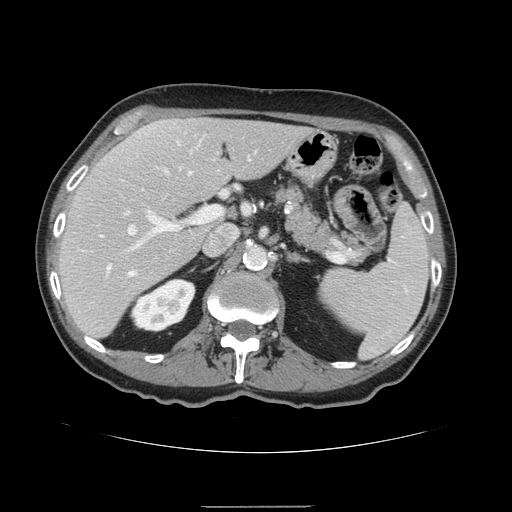
Contrast-enhanced abdominal CT, one axial slice. Slice 91 of 168 in the series (ordered by position). Intravenous contrast given. Soft-tissue window (W 400 / L 40 HU). 512 × 512 image matrix, field of view 386 × 386 mm. Male patient, age 74 years. Case-level facts recorded for this patient, not image findings: diagnosis: colorectal cancer liver metastases, imaged before liver resection; multiple liver metastases: no; largest metastasis: 14.5 cm; chemotherapy before resection: no.
Structures marked on this image (outlined manually by an expert reader):
- hepatic veins: bounding box <128,158,250,275> (left, top, right, bottom; pixels)
- liver: <59,119,312,339>
- planned liver remnant (the part of the liver to remain after resection): <58,119,313,339>
- portal vein (with intrahepatic branches): <78,196,222,271>